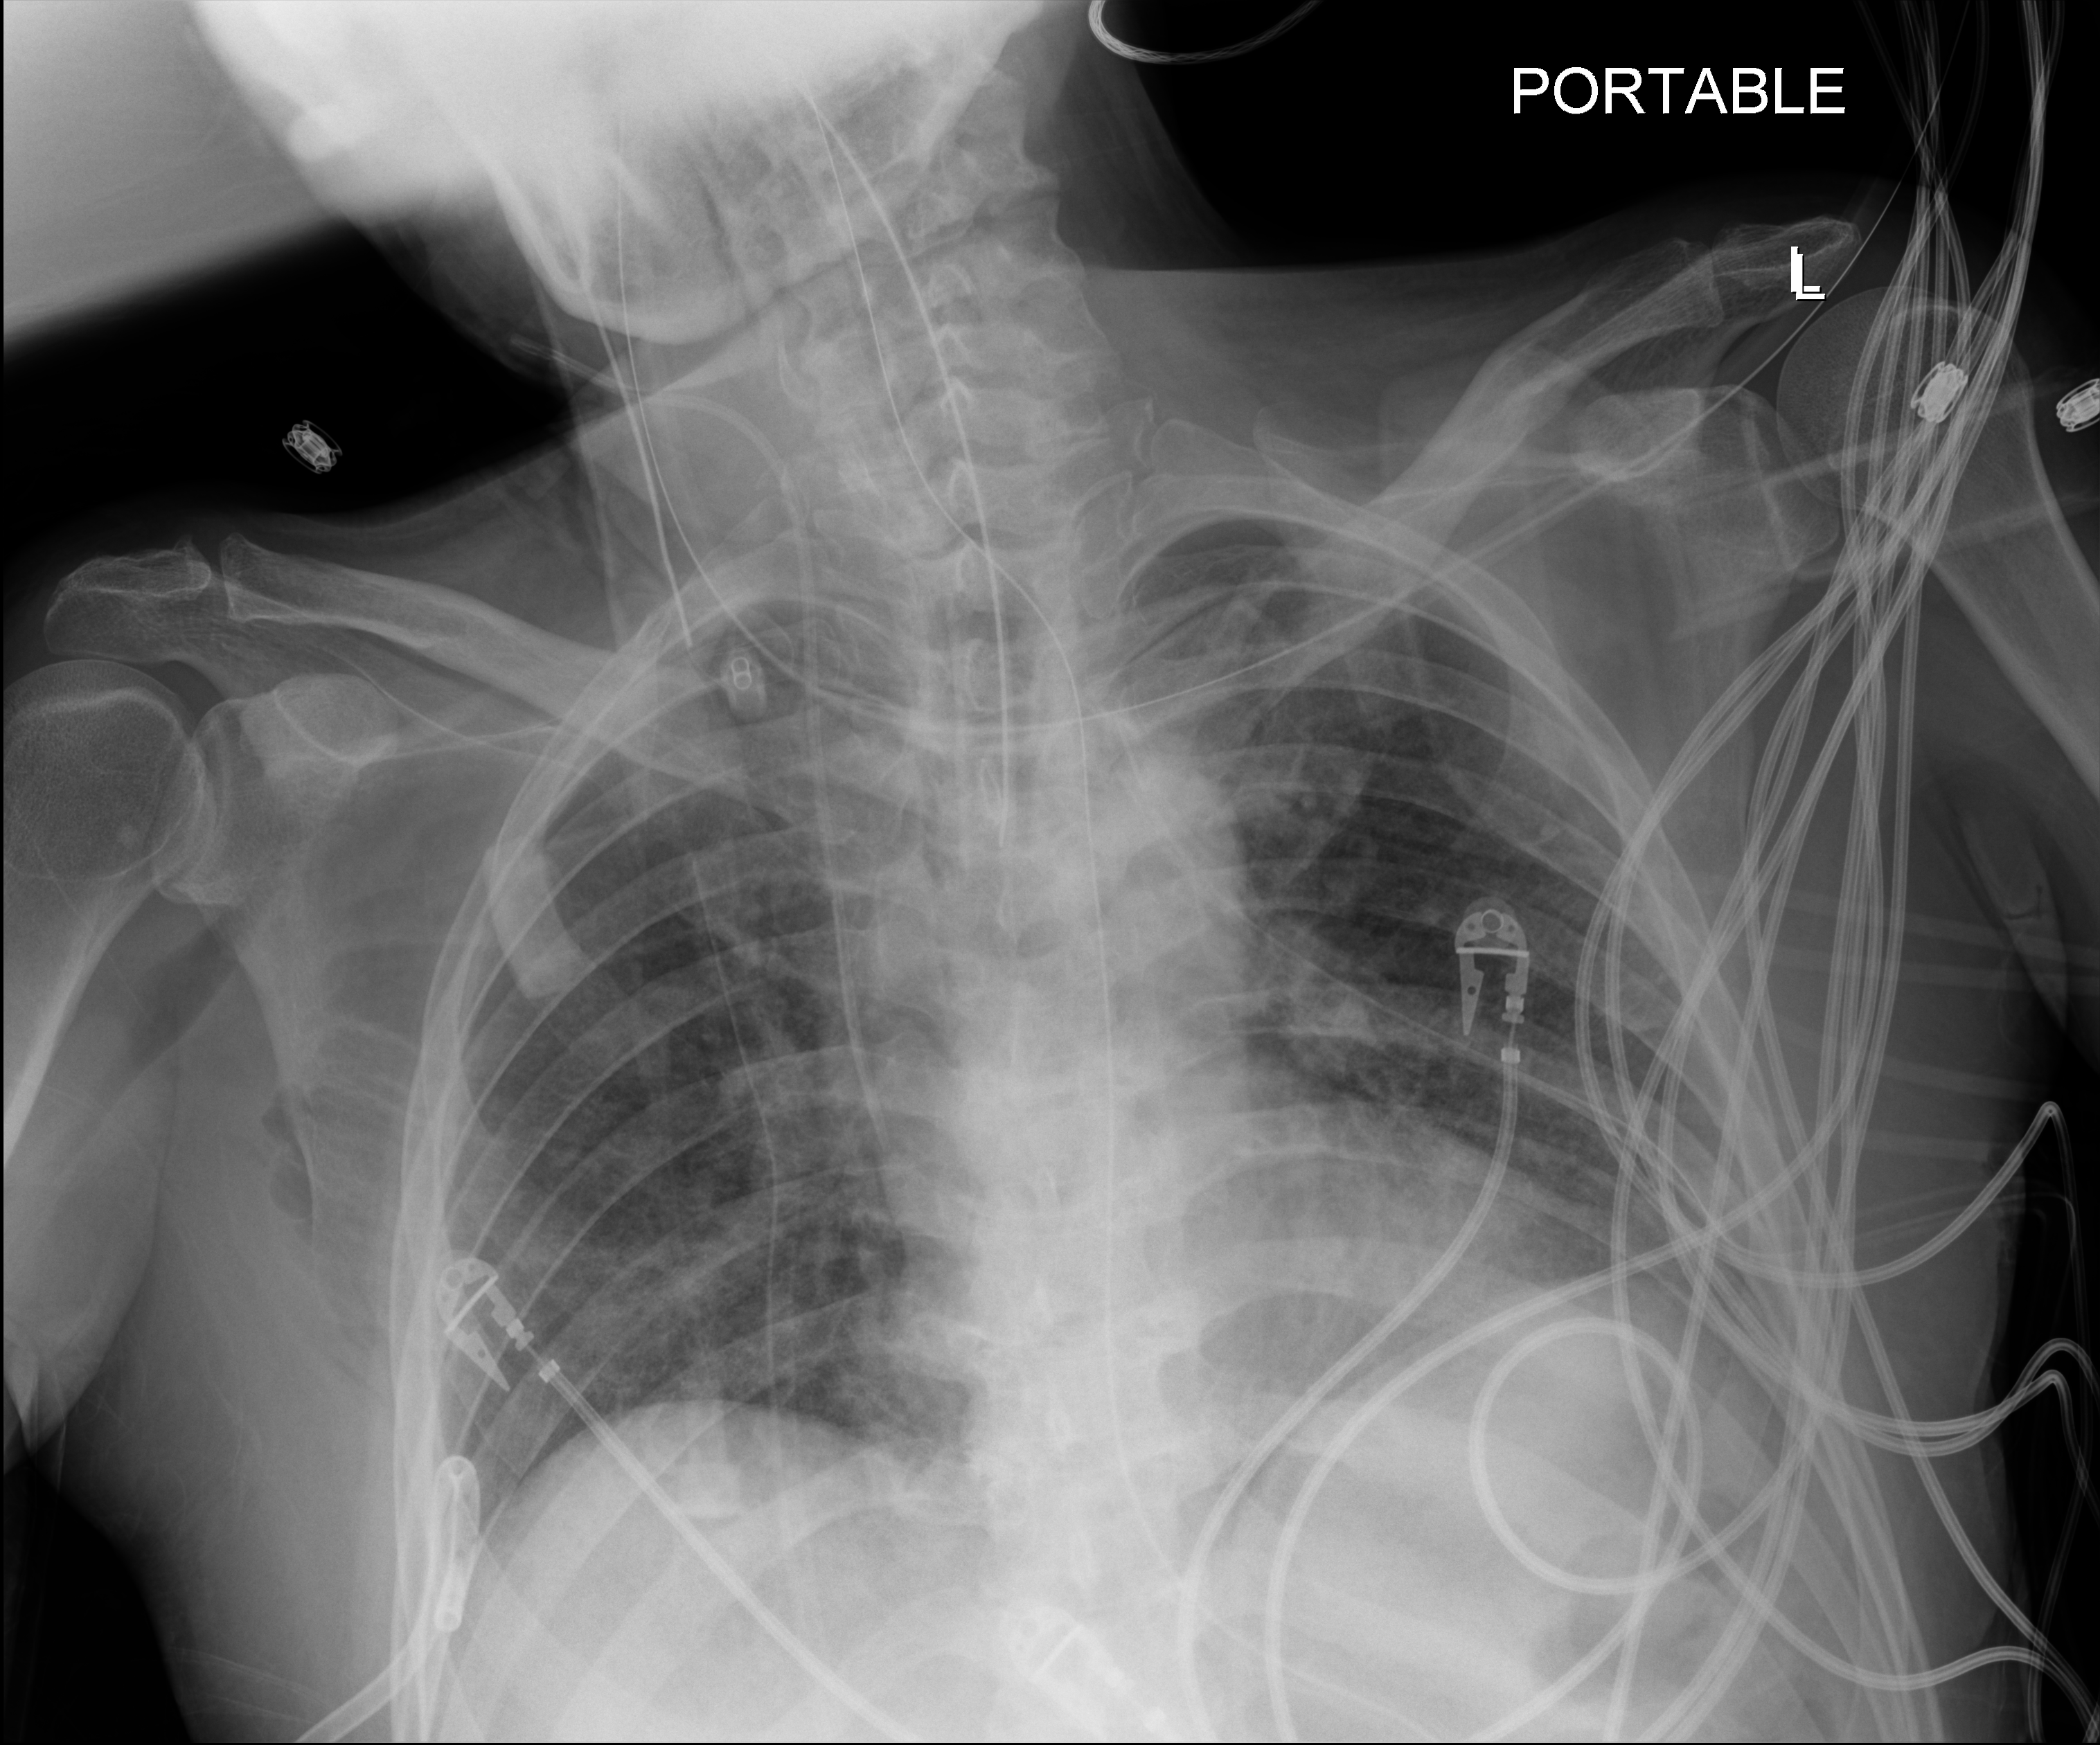
Chest X-ray (portable). Patient hospitalised with COVID-19; male, aged 18–59 years.
From the hospital-stay record, not from the radiograph (when in the stay this image was taken is not recorded): admitted to intensive care during this hospital stay: yes; mechanically ventilated during this hospital stay: yes.